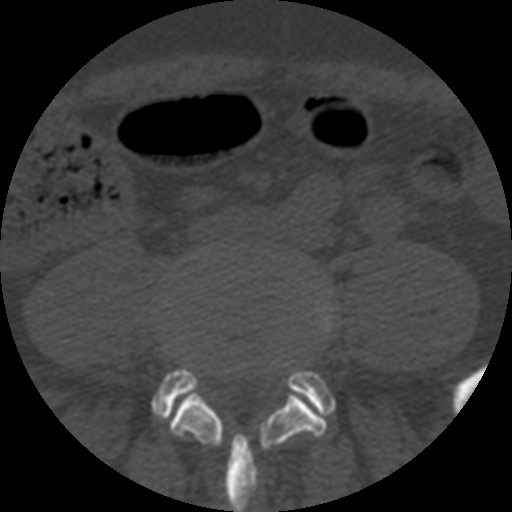
CT including the spine, one axial slice; slice 79 of 508 in the series (ordered by position); reconstruction kernel STANDARD; 120 kVp; bone window (W 1800 / L 400 HU); 512 × 512 image matrix, field of view 160 × 160 mm. Patient age 57 years. From the clinical record (not read from this slice): primary cancer: prostate.
Annotated regions visible in this slice (semi-automatic segmentation, software-assisted and operator-edited):
- L4 vertebra: bounding box [x1, y1, x2, y2] px = [171, 286, 335, 512]
- L5 vertebra: [153, 368, 334, 421]